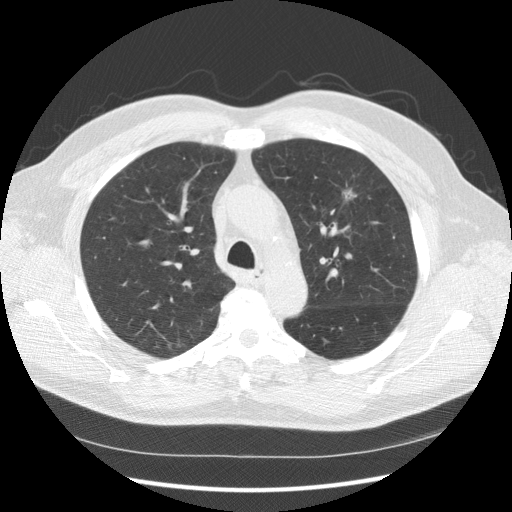
Low-dose screening chest CT, one axial slice; slice 111 of 157 in the series (ordered by position); reconstruction kernel STANDARD; 120 kVp; lung window (W 1500 / L -600 HU); 2.5 mm slice thickness; 512 × 512 image matrix, field of view 370 × 370 mm.
Structures marked on this image (expert manual segmentation):
- lesion 1 (tumor, upper lobe of left lung): bounding box (x1, y1, x2, y2) in pixels: (344, 190, 355, 200)